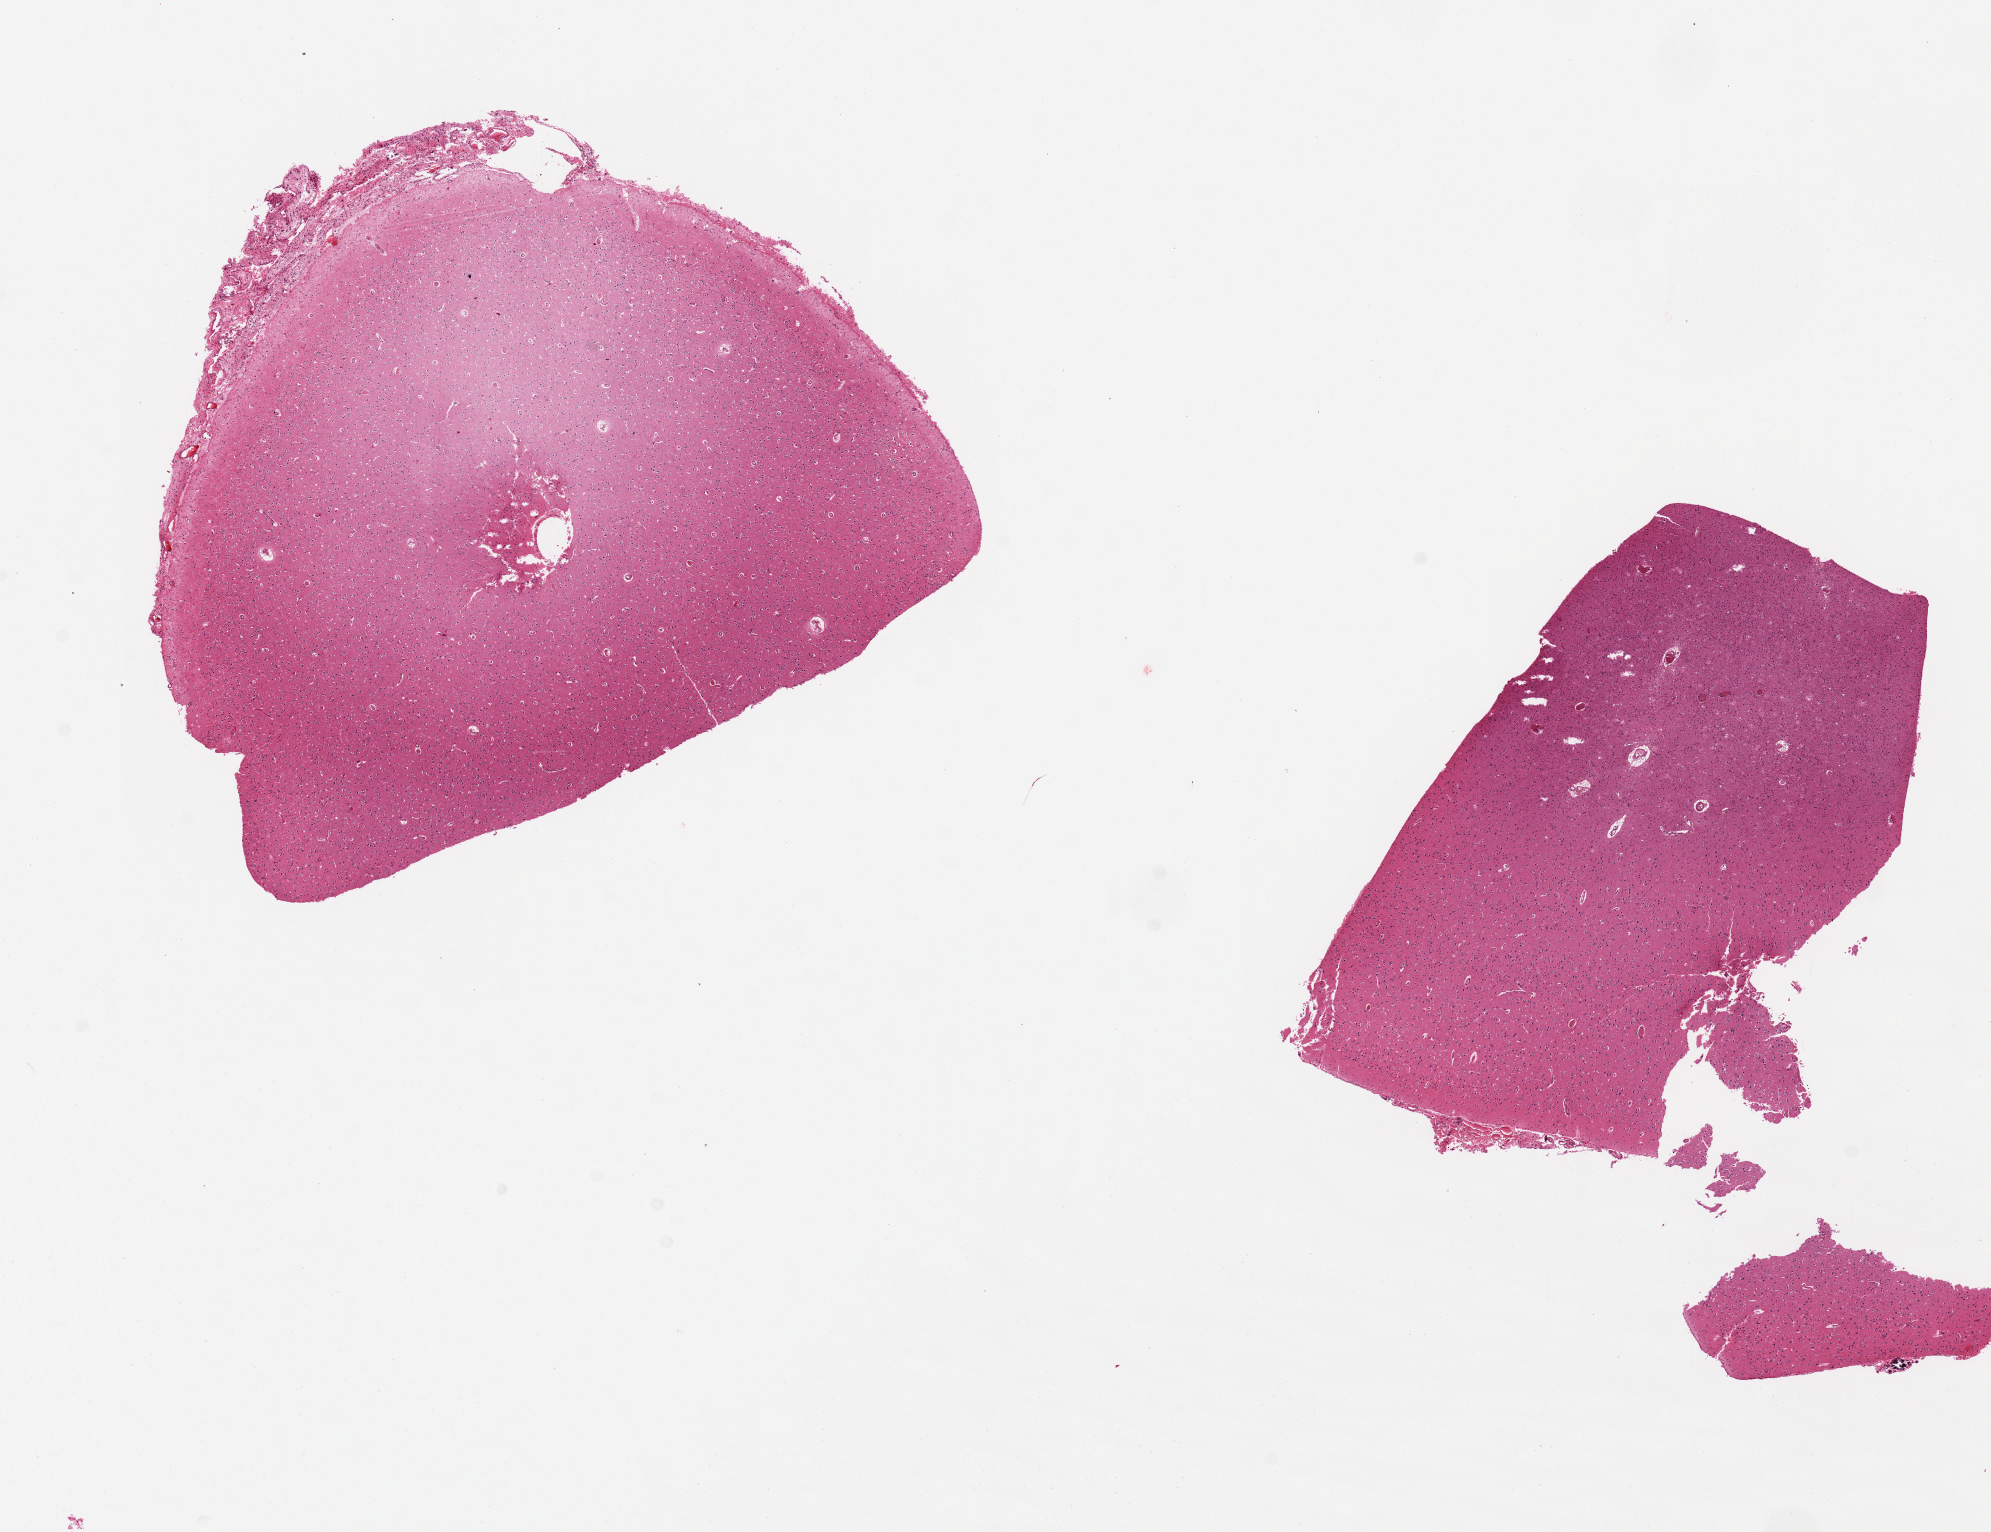
H&E whole-slide image, shown as a low-resolution overview of the whole scanned area (about 15.8 x 12.1 mm, slide scanned at 20x); PAXgene-fixed paraffin-embedded (PFPE) section; section of cerebral cortex (target tissue); donor tissue sample. Donor sex: female.
Reviewer comment on this tissue sample: Two pieces: 5x6.5mm. Slight fractures.